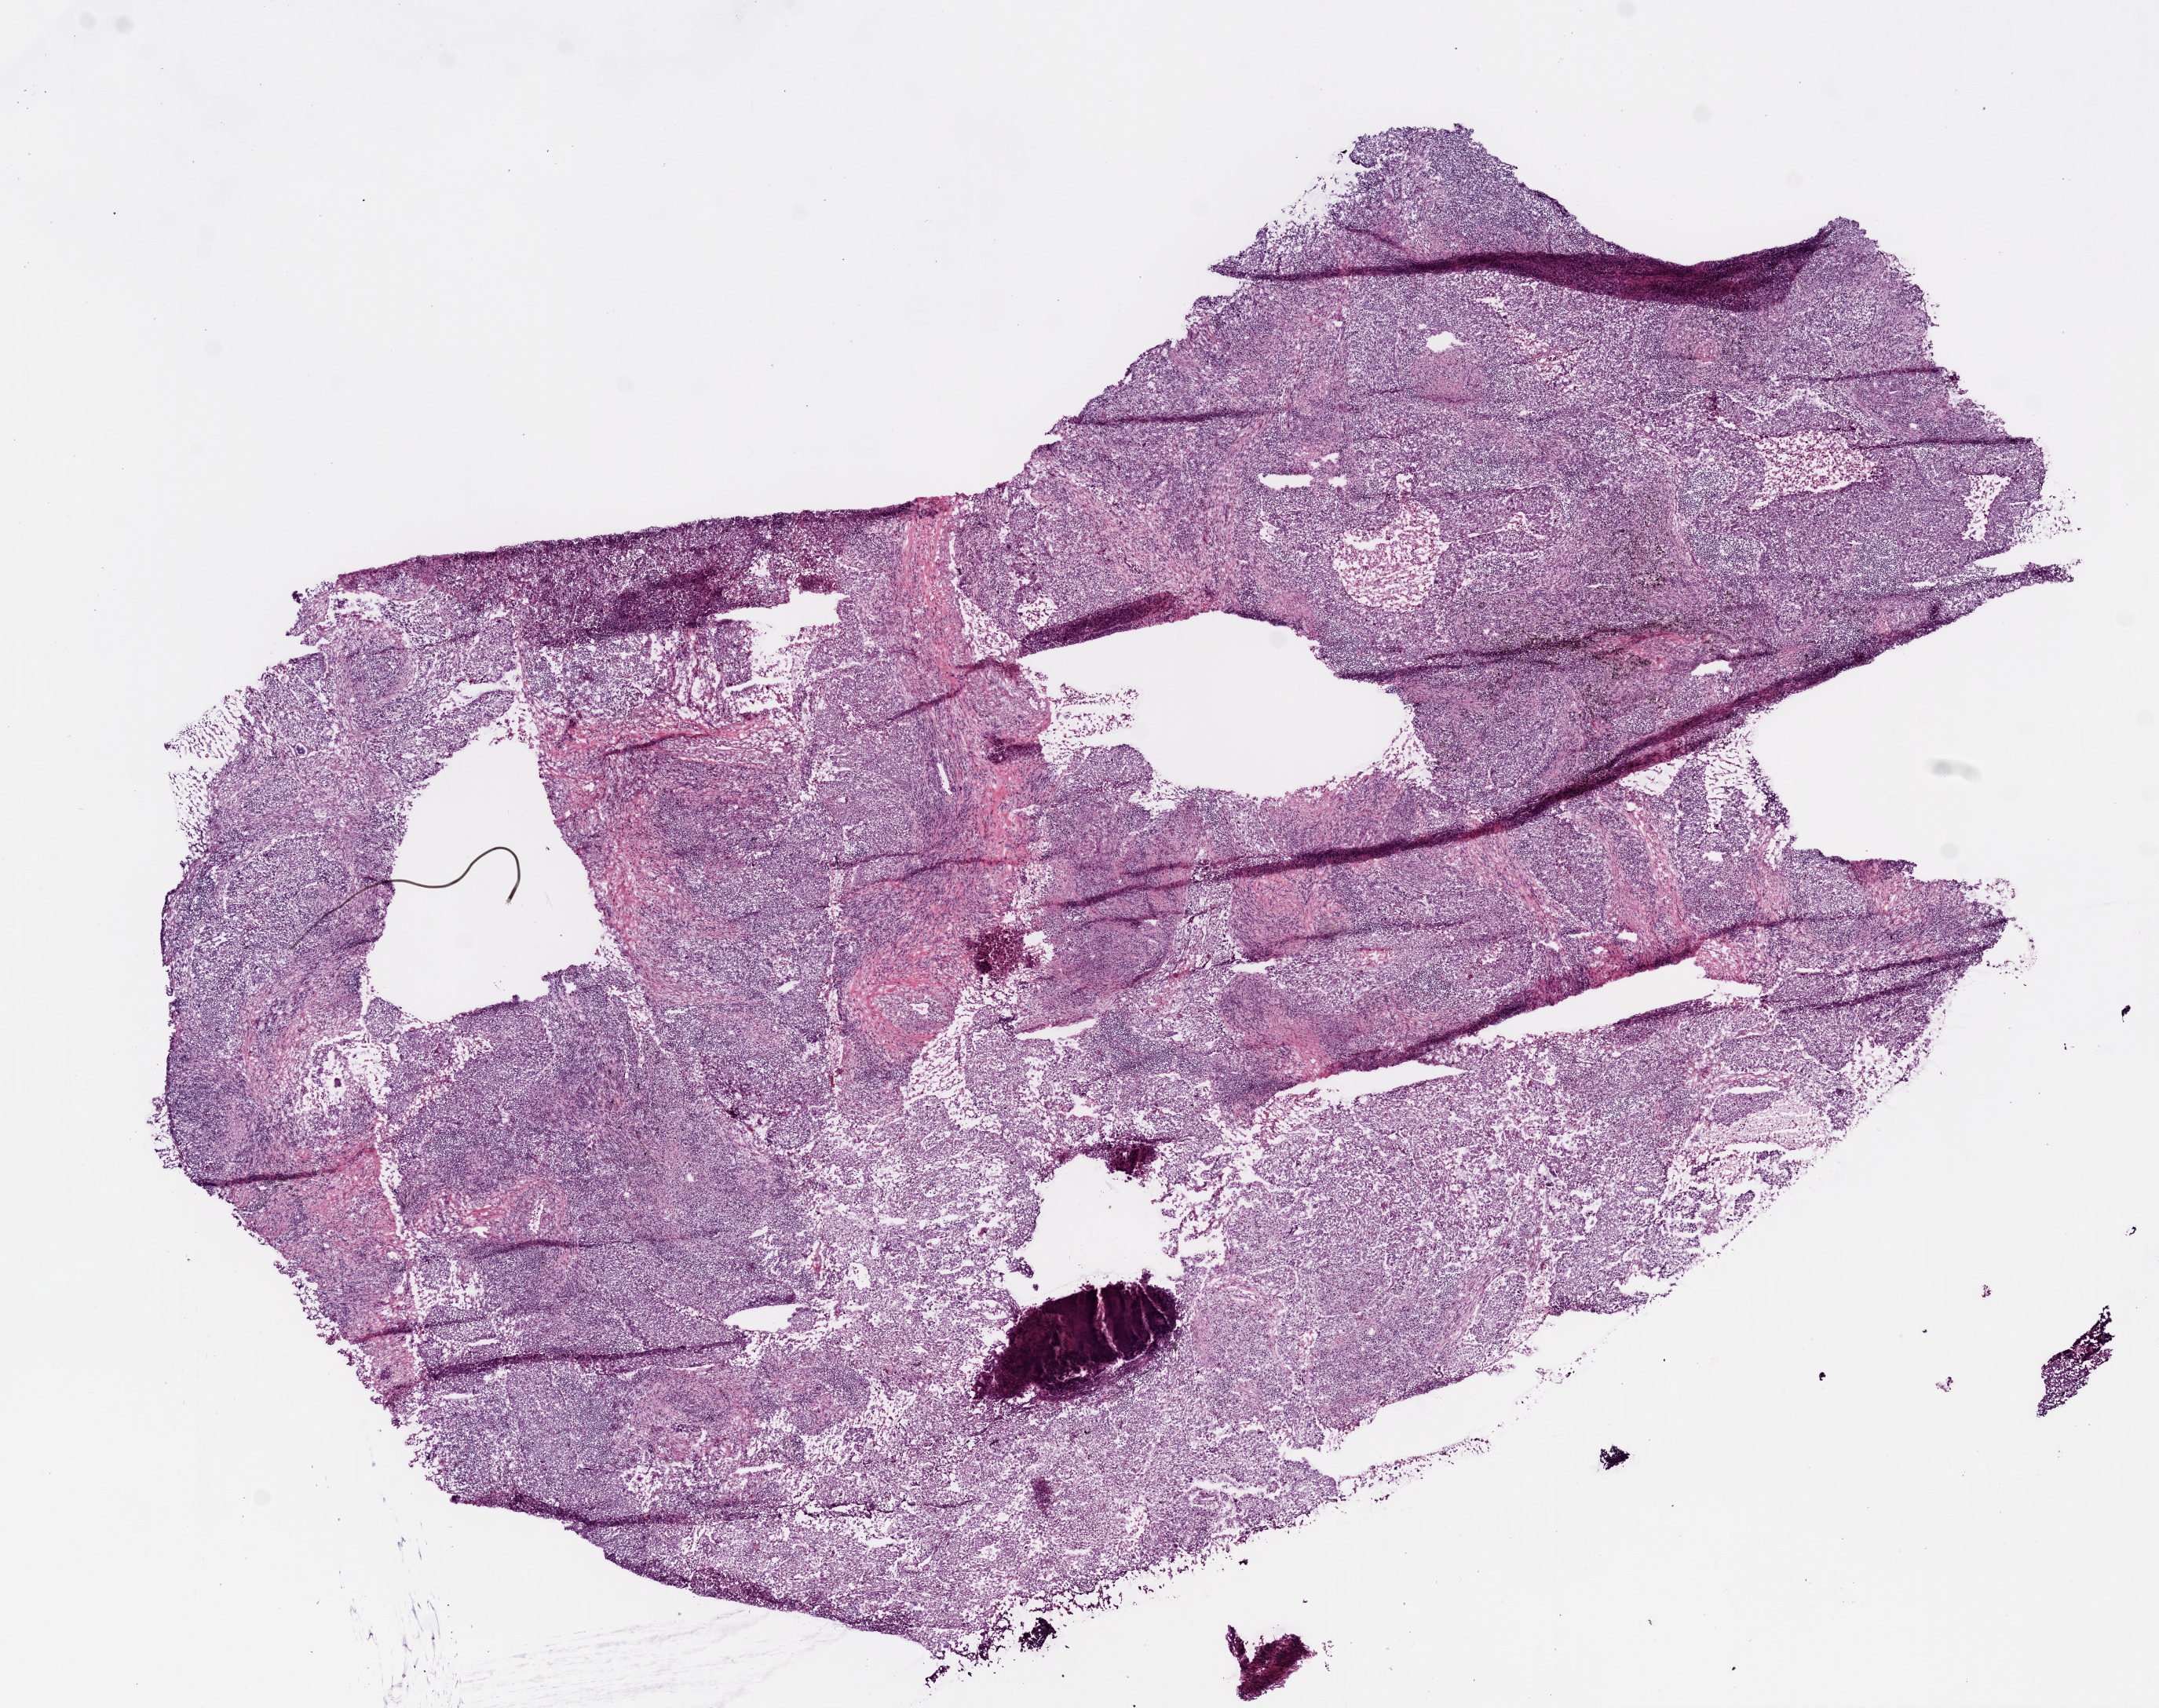
Hematoxylin and eosin (H&E) stained whole-slide image, shown as a low-resolution overview of the whole scanned area (about 11.0 x 8.7 mm, from a 20x scan), frozen section from the bottom of the tissue portion, lung, primary tumour sample. Patient: male, age at initial diagnosis 74 years. Composition of this section per pathologist review: tumour cells 75%, tumour nuclei 70%, normal cells 0%, stromal cells 15%, necrosis 10%.
• TNM: T1 N0 M0
• AJCC pathologic stage: IA
• laterality: left
• pathologic diagnosis: Squamous cell carcinoma, NOS (lower lobe, lung)